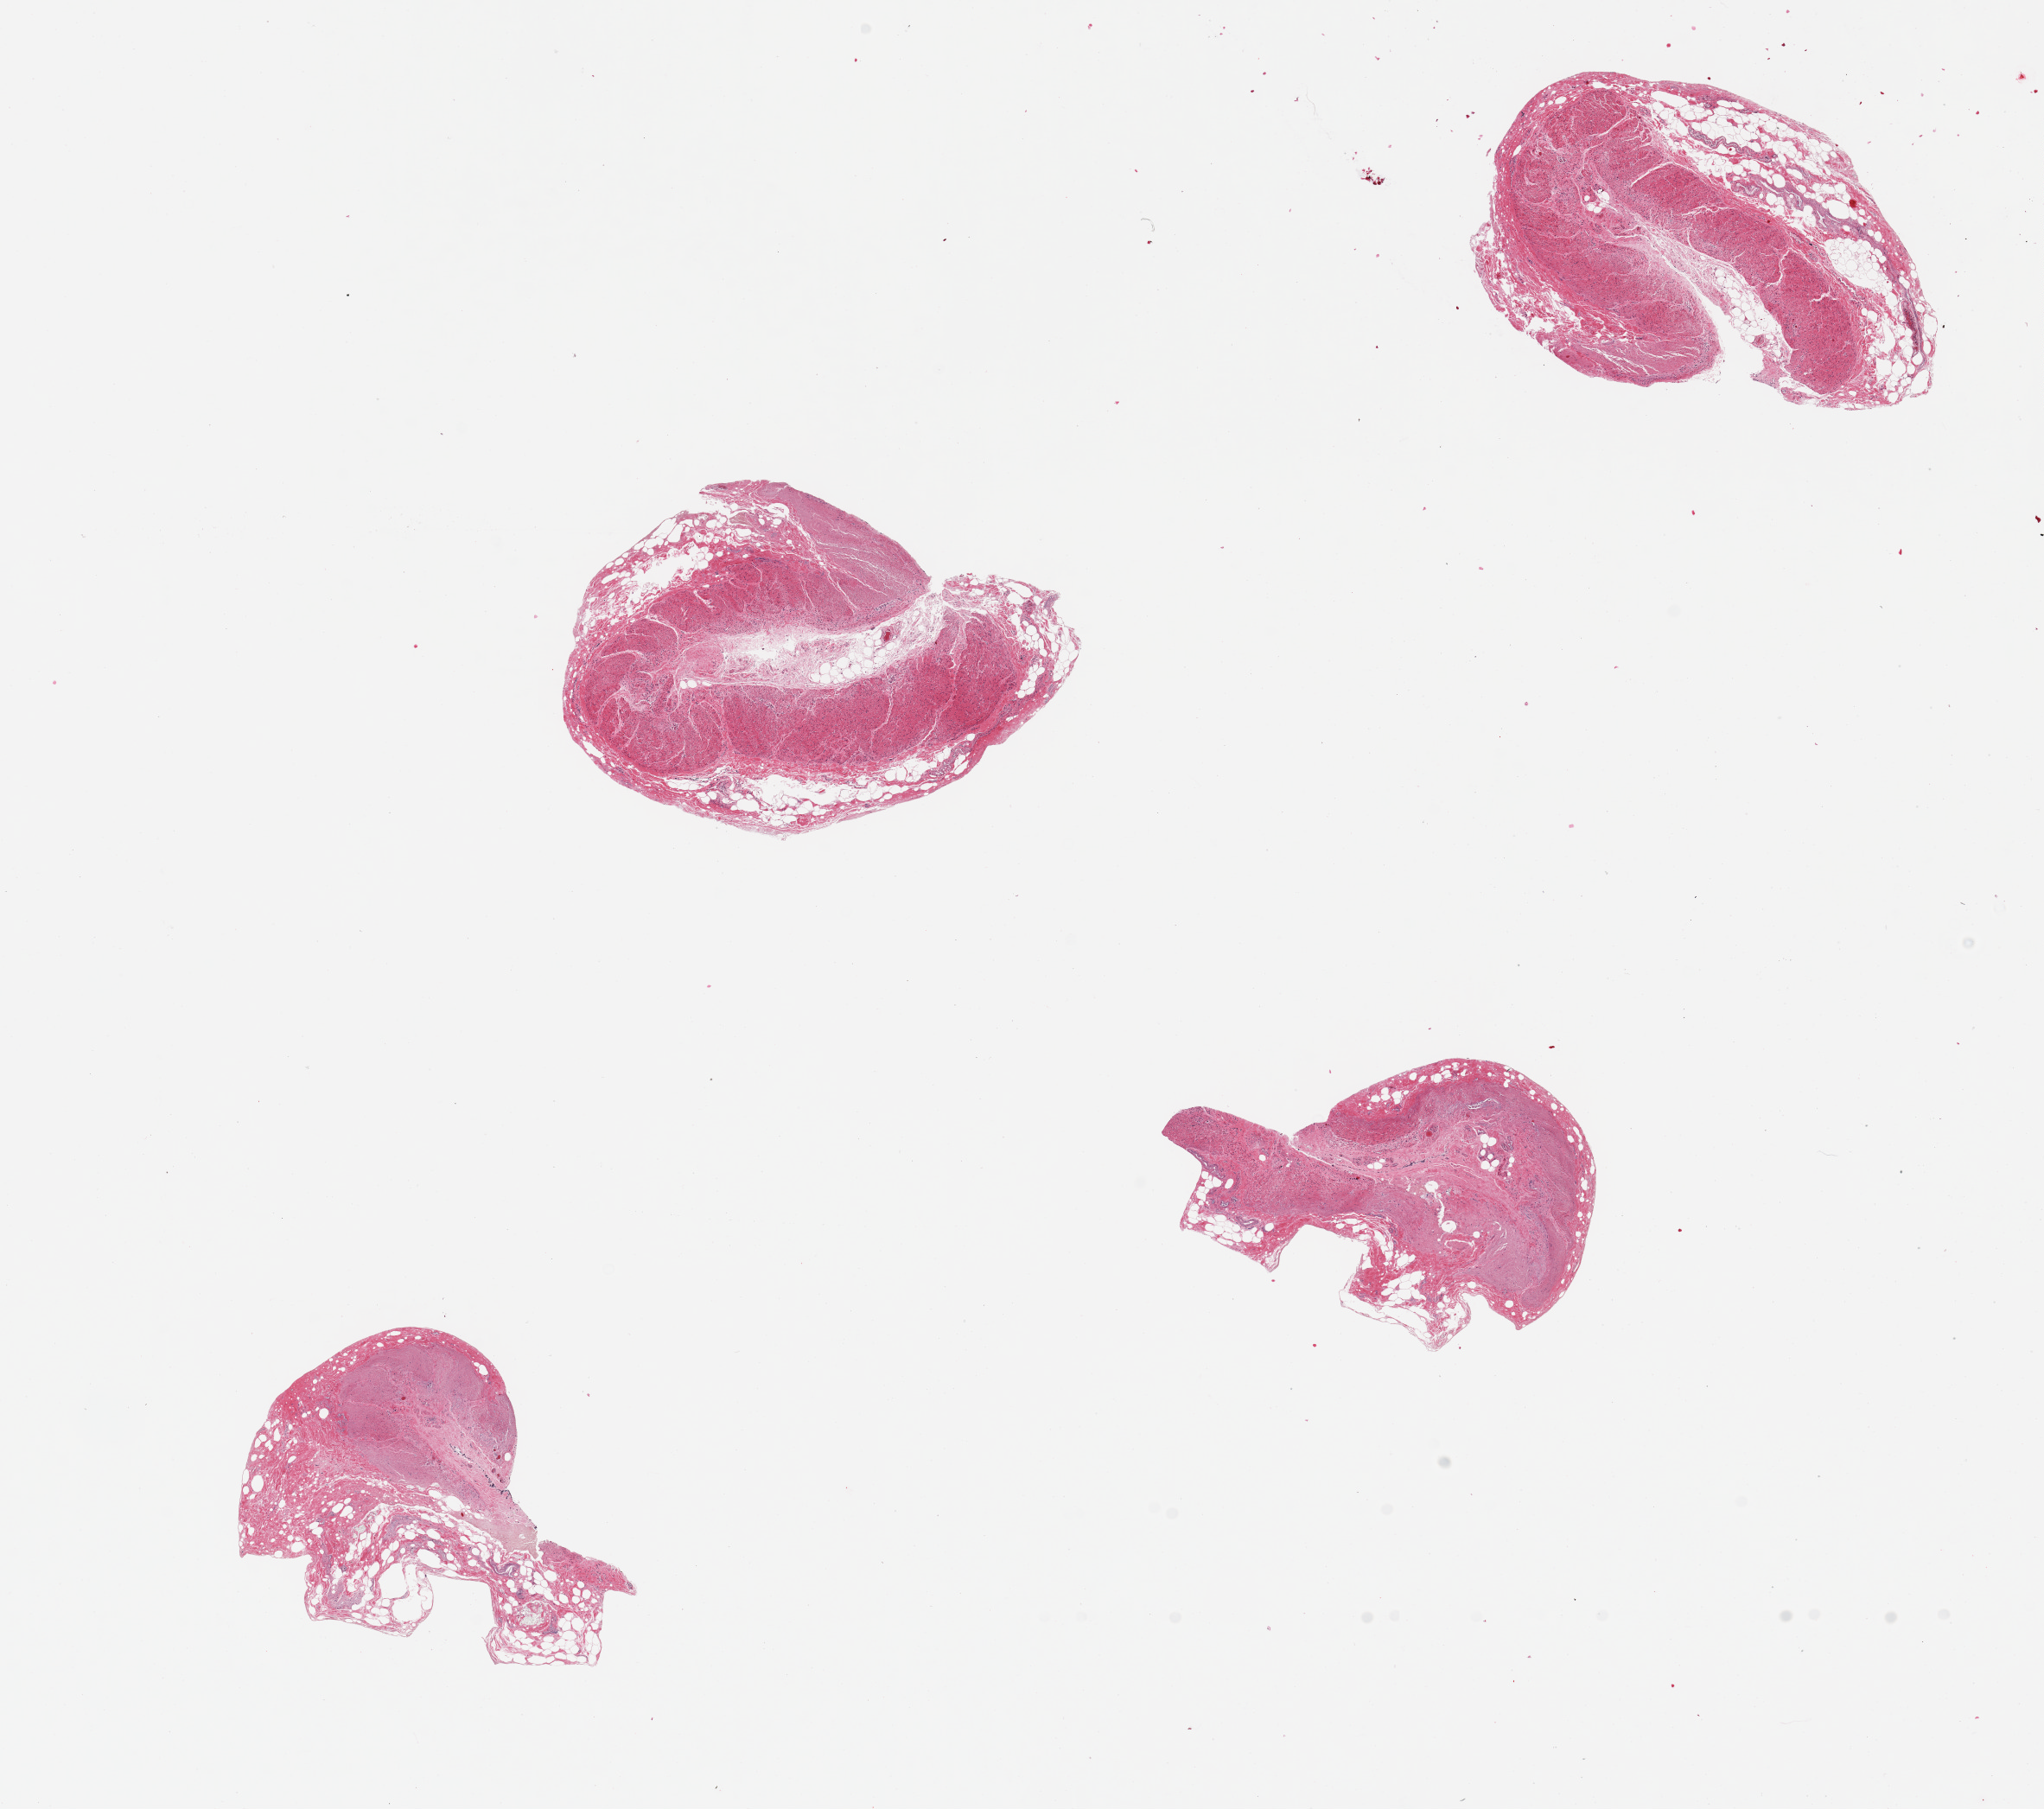
Haematoxylin and eosin whole-slide image, brightfield, low-resolution overview of the scanned area, about 18.7 x 16.6 mm (from a 20x scan). PAXgene-fixed, paraffin-embedded tissue. Sampled site (target tissue): transverse colon. Donor tissue sample. Donor: female.
Pathologist's review note for this sample: 4 pieces; all muscle, no mucosa.